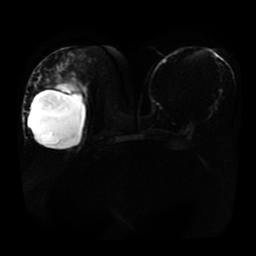
Breast MRI, one axial slice. Slice 19 of 41 in the series (ordered by position). Diffusion-weighted series; image 2 of 4 stored at this slice position (different b-values; order by instance number). 1.5 T. 5 mm slice thickness. 256 × 256 image matrix, field of view 360 × 360 mm. Female patient.
Outlined on this slice (outlined manually by an expert reader):
- tumour on diffusion-weighted imaging: bounding box [x1, y1, x2, y2] px = [54, 79, 84, 94]